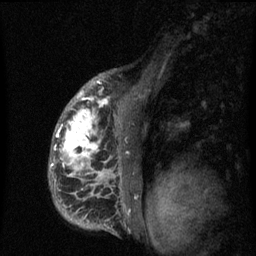
Breast MRI (dynamic contrast-enhanced), one sagittal slice; slice 46 of 60 in the series (ordered by position); dynamic contrast-enhanced series, image 2 of 3 at this slice position (ordered by acquisition); 1.5 T; TE 4.2 ms, TR 8 ms; 256 × 256 image matrix, field of view 190 × 190 mm. Female patient, age 50 years.
Annotated regions visible in this slice (semi-automatic segmentation, software-assisted and operator-edited):
- analysis volume of interest (the breast-tissue region the enhancement analysis was run in; not a lesion): box from (x=48, y=90) to (x=142, y=216) px
- tumour enhancement mask (voxels above the 70 % enhancement threshold inside the analysis volume of interest): (x=50, y=91)–(x=125, y=206)